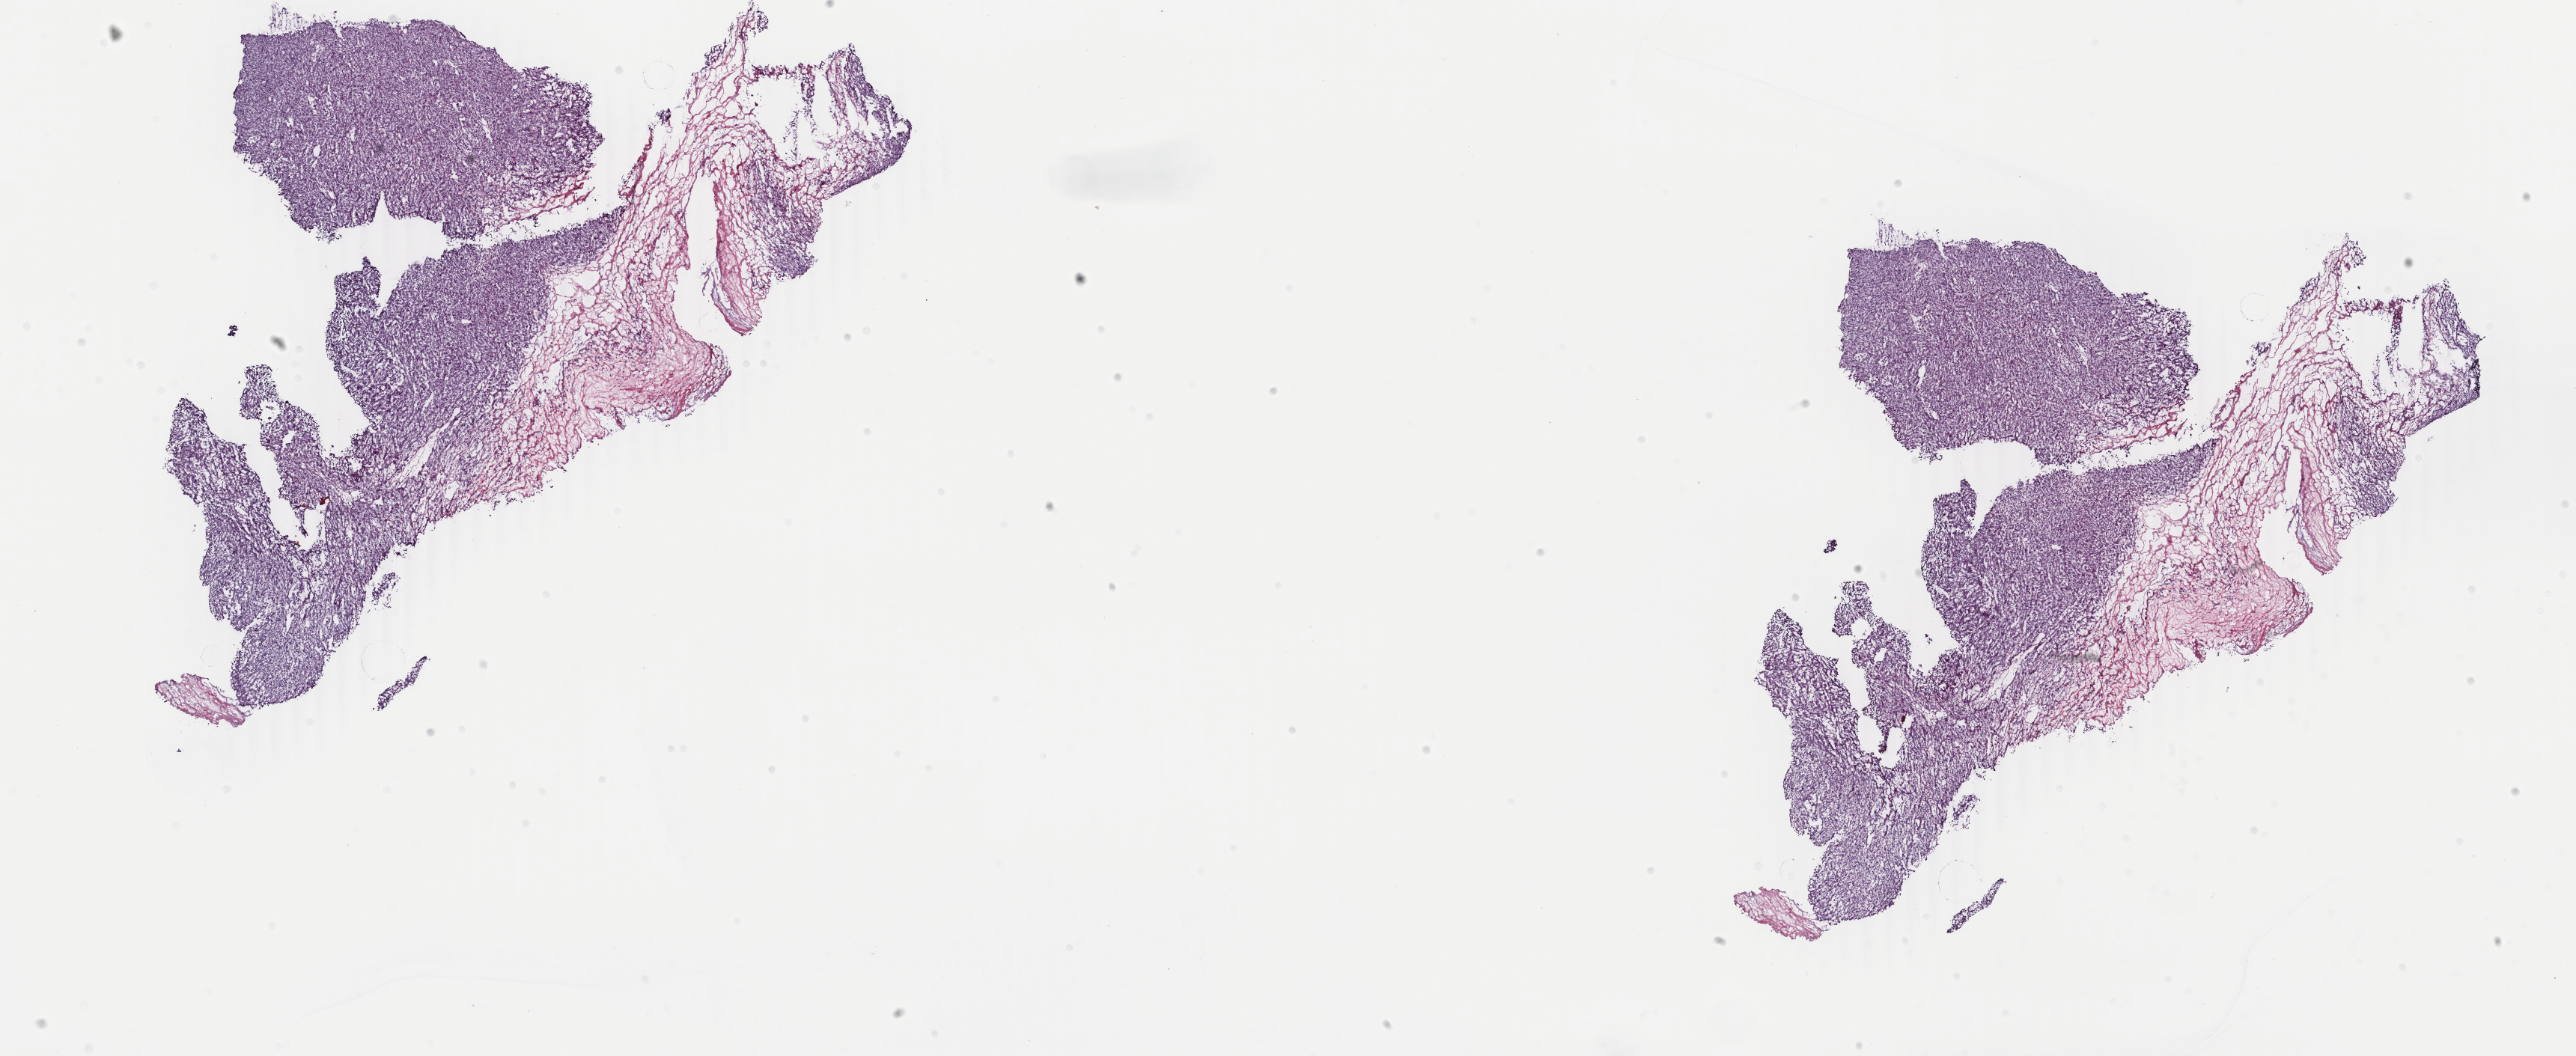
Hematoxylin and eosin (H&E) stained whole-slide image — a low-resolution overview of the entire scanned area, about 27.4 x 11.2 mm. Frozen section from the top of the tissue portion. Primary tumour sample from the adrenal cortex. Male, age 63 years at initial diagnosis. Composition of this section per pathologist review: tumour cells 95%, tumour nuclei 80%, normal cells 5%, stromal cells 0%, necrosis 0%. Infiltration values recorded for this section: lymphocyte infiltration 2%, monocyte infiltration 0%, neutrophil infiltration 0%.
Histologic diagnosis: Adrenal cortical carcinoma (cortex of adrenal gland).